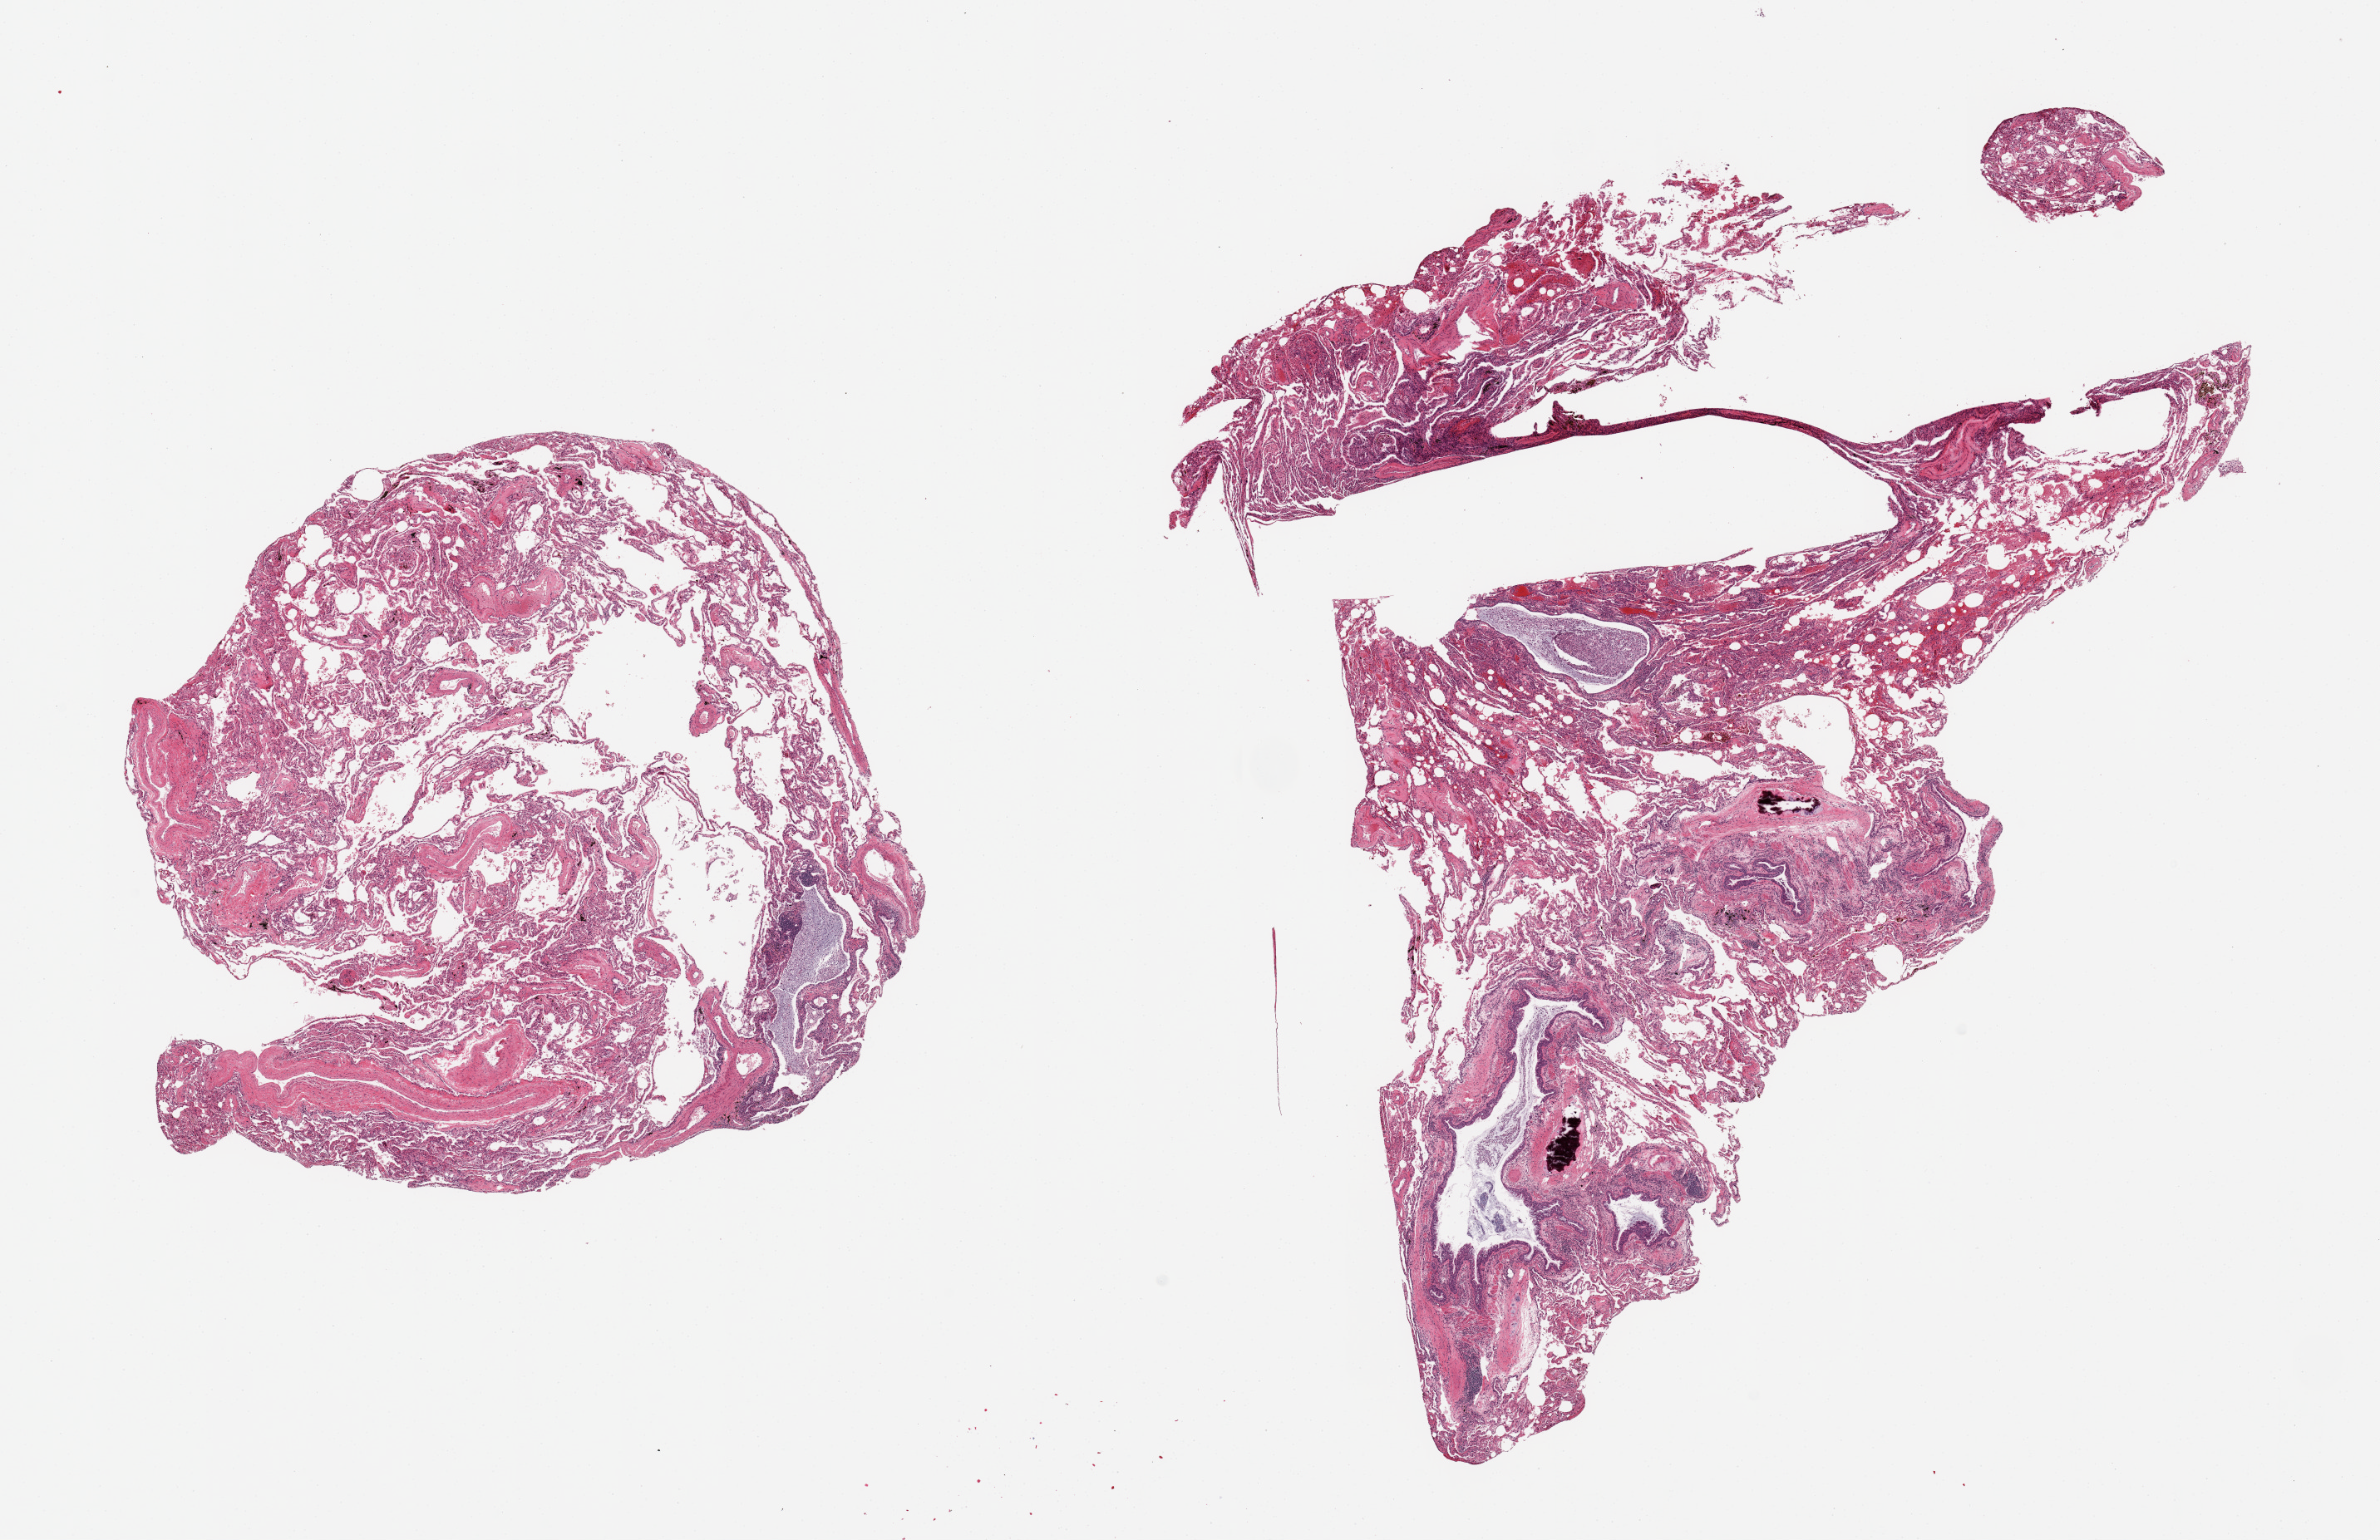
Whole-slide image, haematoxylin and eosin stain, brightfield — whole scanned area (about 22.6 x 14.7 mm) shown as a low-resolution overview. PAXgene-fixed paraffin-embedded (PFPE) section. Section of lung (target tissue). Donor tissue sample. Donor sex: female.
- review note (as recorded): 2 pieces; bronchiectasis, emphysema, fibrosis, bronchitis